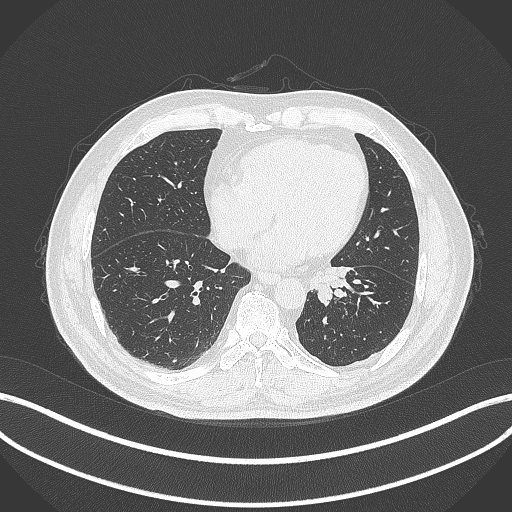
Chest CT, one axial slice. Slice 91 of 312 in the series (ordered by position). Reconstruction kernel B70f. 120 kVp. Lung window (W 1500 / L -600 HU). 1 mm slice thickness. 512 × 512 image matrix, field of view 400 × 400 mm. Patient: male, 71 years. Case-level facts recorded for this patient, not image findings: clinical TNM (as recorded): T1b N0 M0.
Outlined on this slice (bounding box drawn by a radiologist):
- lung tumour (recorded histology: squamous cell carcinoma): box from (x=310, y=267) to (x=355, y=306) px